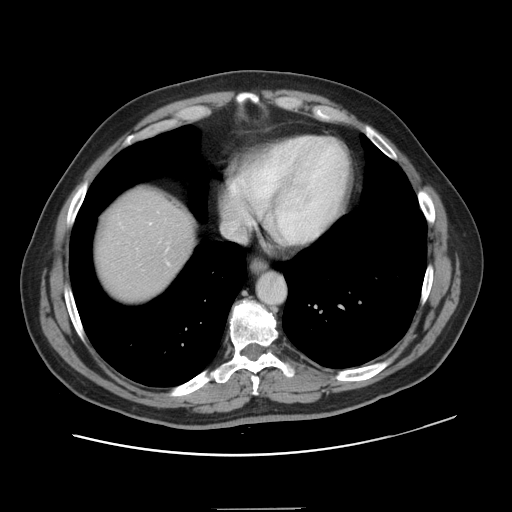
Contrast-enhanced abdominal CT, one axial slice; slice 135 of 143 in the series (ordered by position); 120 kVp; intravenous contrast given; soft-tissue window (W 400 / L 40 HU); 2.5 mm slice thickness; 512 × 512 image matrix, field of view 402 × 402 mm. Male patient, age 62 years. From the clinical record (not read from this slice): diagnosis: colorectal cancer liver metastases, imaged before liver resection; multiple liver metastases: yes; largest metastasis: 2.7 cm.
Annotated regions visible in this slice (manually delineated by an expert):
- liver: bounding box [x1, y1, x2, y2] px = [97, 191, 191, 301]
- planned liver remnant (the part of the liver to remain after resection): [98, 191, 191, 299]